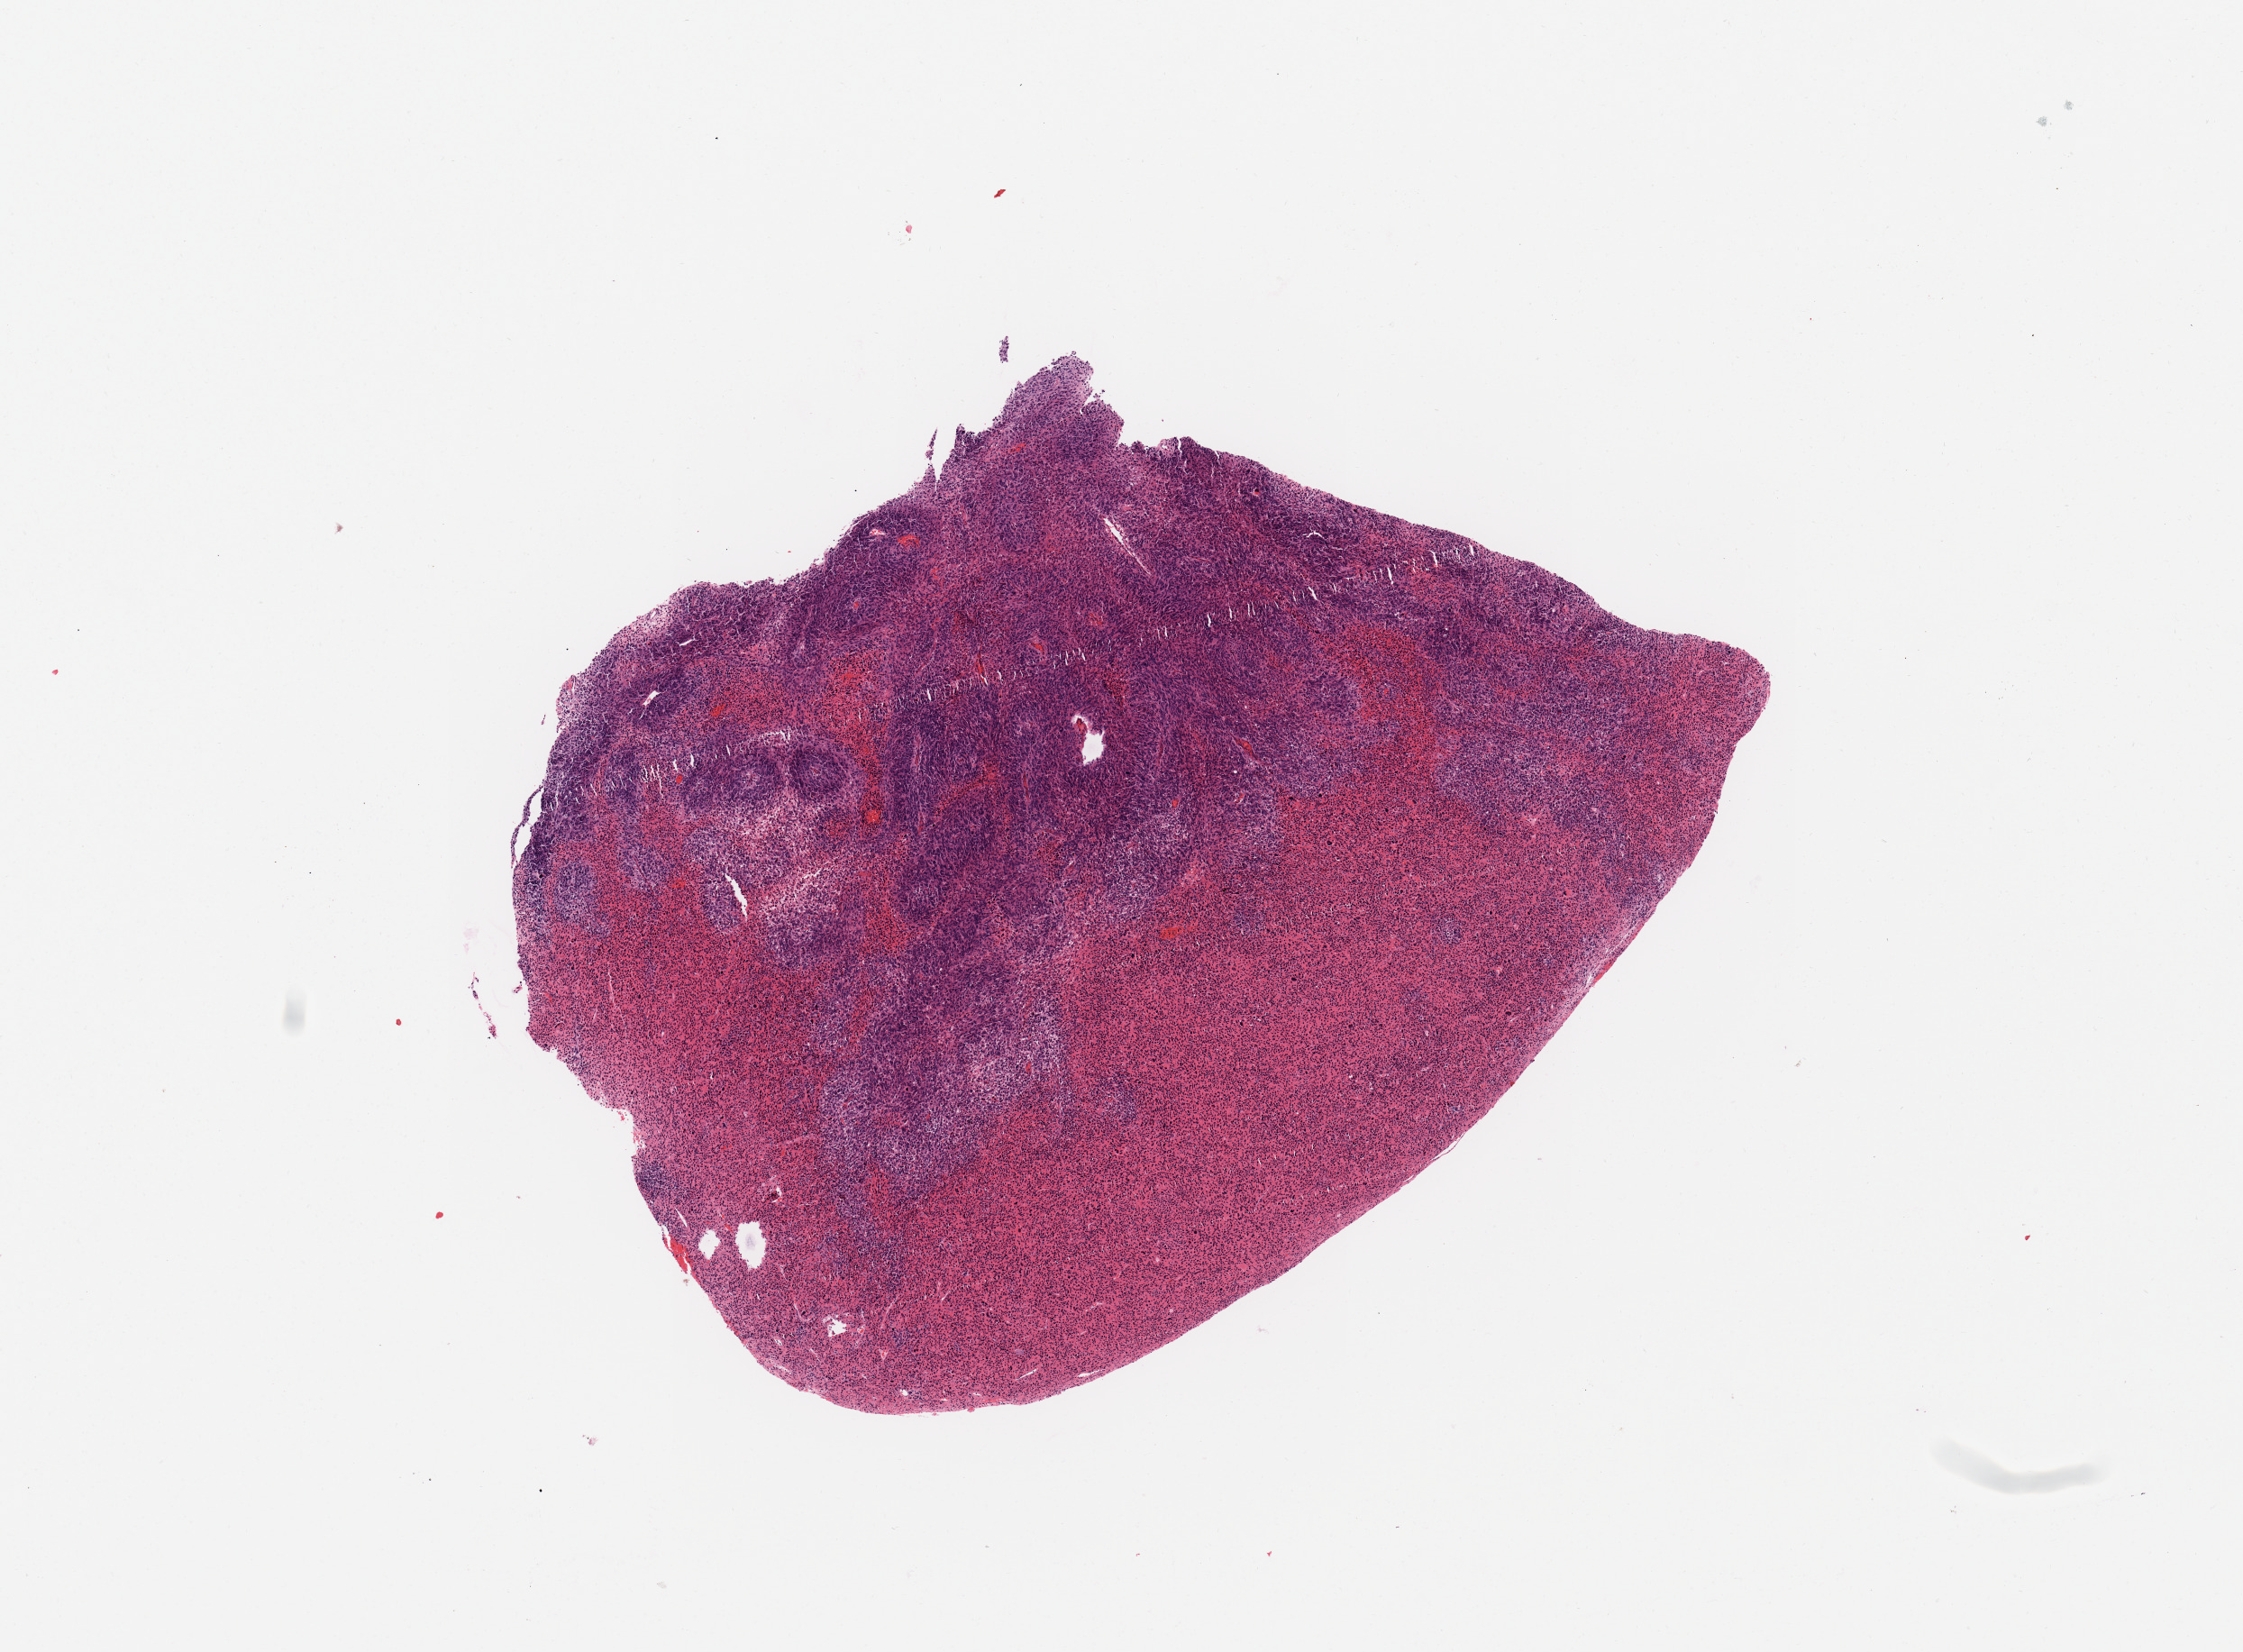
Digitized Hematoxylin and eosin (H&E) stained tissue section (whole slide), whole scanned area (about 9.8 x 7.2 mm, slide scanned at 20x) shown as a low-resolution overview, tumour tissue sample. Patient: male, age 56 years.
Primary tumour site (as recorded): retroperitoneum. Patient diagnosis (cohort enrolment): sarcoma (site not recorded at cohort level).